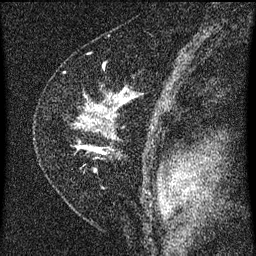
Breast MRI (dynamic contrast-enhanced), one sagittal slice. Slice 43 of 60 in the series (ordered by position). Dynamic contrast-enhanced series, image 2 of 3 at this slice position (ordered by acquisition). 1.5 T. TE 4.2 ms, TR 8 ms. 2 mm slice thickness. 256 × 256 image matrix, field of view 180 × 180 mm. Patient: female, 47 years.
Annotated regions visible in this slice (semi-automatic segmentation, software-assisted and operator-edited):
- analysis volume of interest (the breast-tissue region the enhancement analysis was run in; not a lesion): box from (x=46, y=76) to (x=135, y=191) px
- tumour enhancement mask (voxels above the 70 % enhancement threshold inside the analysis volume of interest): (x=79, y=146)–(x=105, y=155)